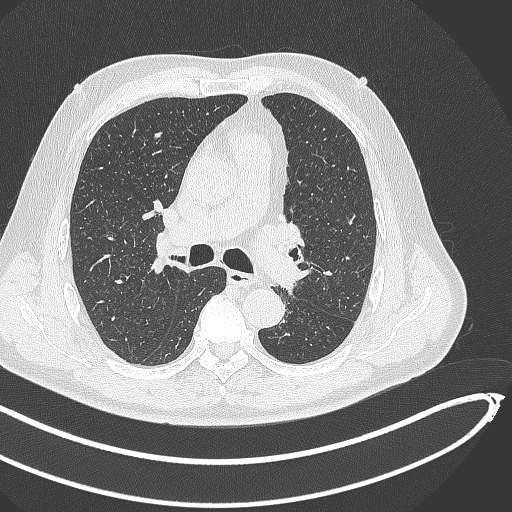
Chest CT, one axial slice. Position 285 of 468 along the scan axis. Reconstruction kernel B70f. Lung window (W 1500 / L -600 HU). 512 × 512 image matrix, field of view 400 × 400 mm. Patient: male, 64 years. Case-level facts recorded for this patient, not image findings: clinical TNM (as recorded): T1c N0 M0; histopathological grade: G2.
Outlined on this slice (rectangle marked by the reading radiologist):
- lung tumour (recorded histology: squamous cell carcinoma): box from (x=276, y=263) to (x=307, y=298) px